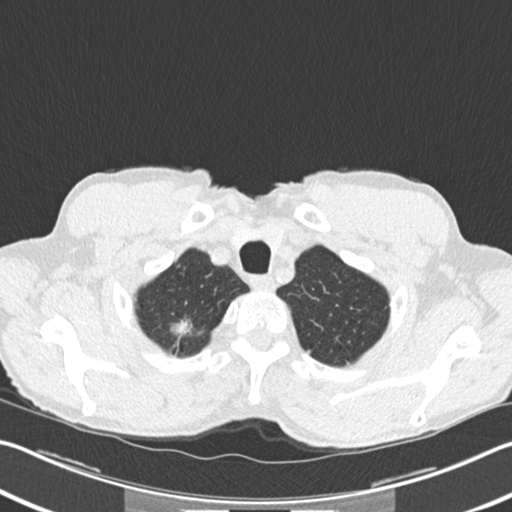
Low-dose screening chest CT, one axial slice; position 202 of 220 along the scan axis; lung window (W 1500 / L -600 HU); 2 mm slice thickness; 512 × 512 image matrix, field of view 342 × 342 mm.
Annotated regions visible in this slice (manually delineated by an expert):
- lesion 1 (tumor, upper lobe of right lung): bounding box [x1, y1, x2, y2] px = [171, 319, 191, 335]